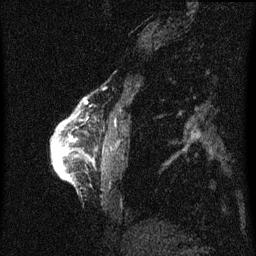
Breast MRI (dynamic contrast-enhanced), one sagittal slice; position 10 of 60 along the scan axis; dynamic contrast-enhanced series, image 2 of 3 at this slice position (ordered by acquisition); 1.5 T; TE 4.2 ms, TR 8 ms; 256 × 256 image matrix. Patient: female, 56 years.
Outlined on this slice (semi-automatically segmented with operator editing):
- analysis volume of interest (the breast-tissue region the enhancement analysis was run in; not a lesion): box from (x=52, y=120) to (x=71, y=181) px
- tumour enhancement mask (voxels above the 70 % enhancement threshold inside the analysis volume of interest): (x=52, y=142)–(x=69, y=179)